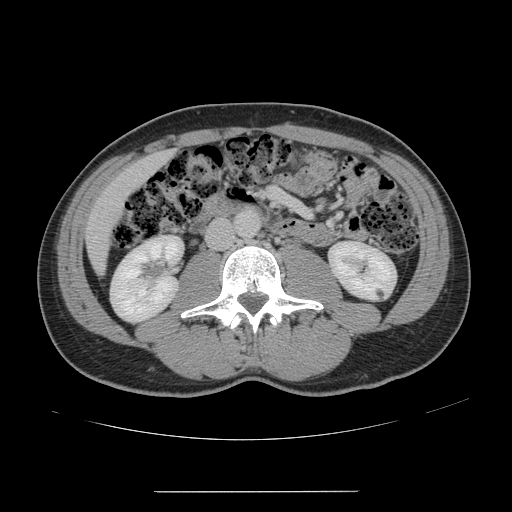
Contrast-enhanced abdominal CT, one axial slice. Slice 39 of 178 in the series (ordered by position). Intravenous contrast given. Soft-tissue window (W 400 / L 40 HU). 2.5 mm slice thickness. 512 × 512 image matrix, field of view 401 × 401 mm. Male patient, age 53 years. Case-level facts recorded for this patient, not image findings: diagnosis: colorectal cancer liver metastases, imaged before liver resection; multiple liver metastases: yes; largest metastasis: 2.4 cm; disease in both lobes: no.
Annotated regions visible in this slice (manually delineated by an expert):
- liver: box from (x=87, y=152) to (x=170, y=271) px